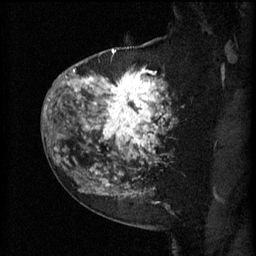
Breast MRI (dynamic contrast-enhanced), one sagittal slice; position 42 of 60 along the scan axis; 3 images stored at this slice position (order not interpretable as contrast timing); 1.5 T; TE 4.2 ms, TR 11 ms; 2 mm slice thickness; 256 × 256 image matrix, field of view 180 × 180 mm. Female patient, age 52 years.
Annotated regions visible in this slice (semi-automatic segmentation, software-assisted and operator-edited):
- analysis volume of interest (the breast-tissue region the enhancement analysis was run in; not a lesion): box from (x=81, y=52) to (x=174, y=157) px
- tumour enhancement mask (voxels above the 70 % enhancement threshold inside the analysis volume of interest): (x=81, y=52)–(x=172, y=157)